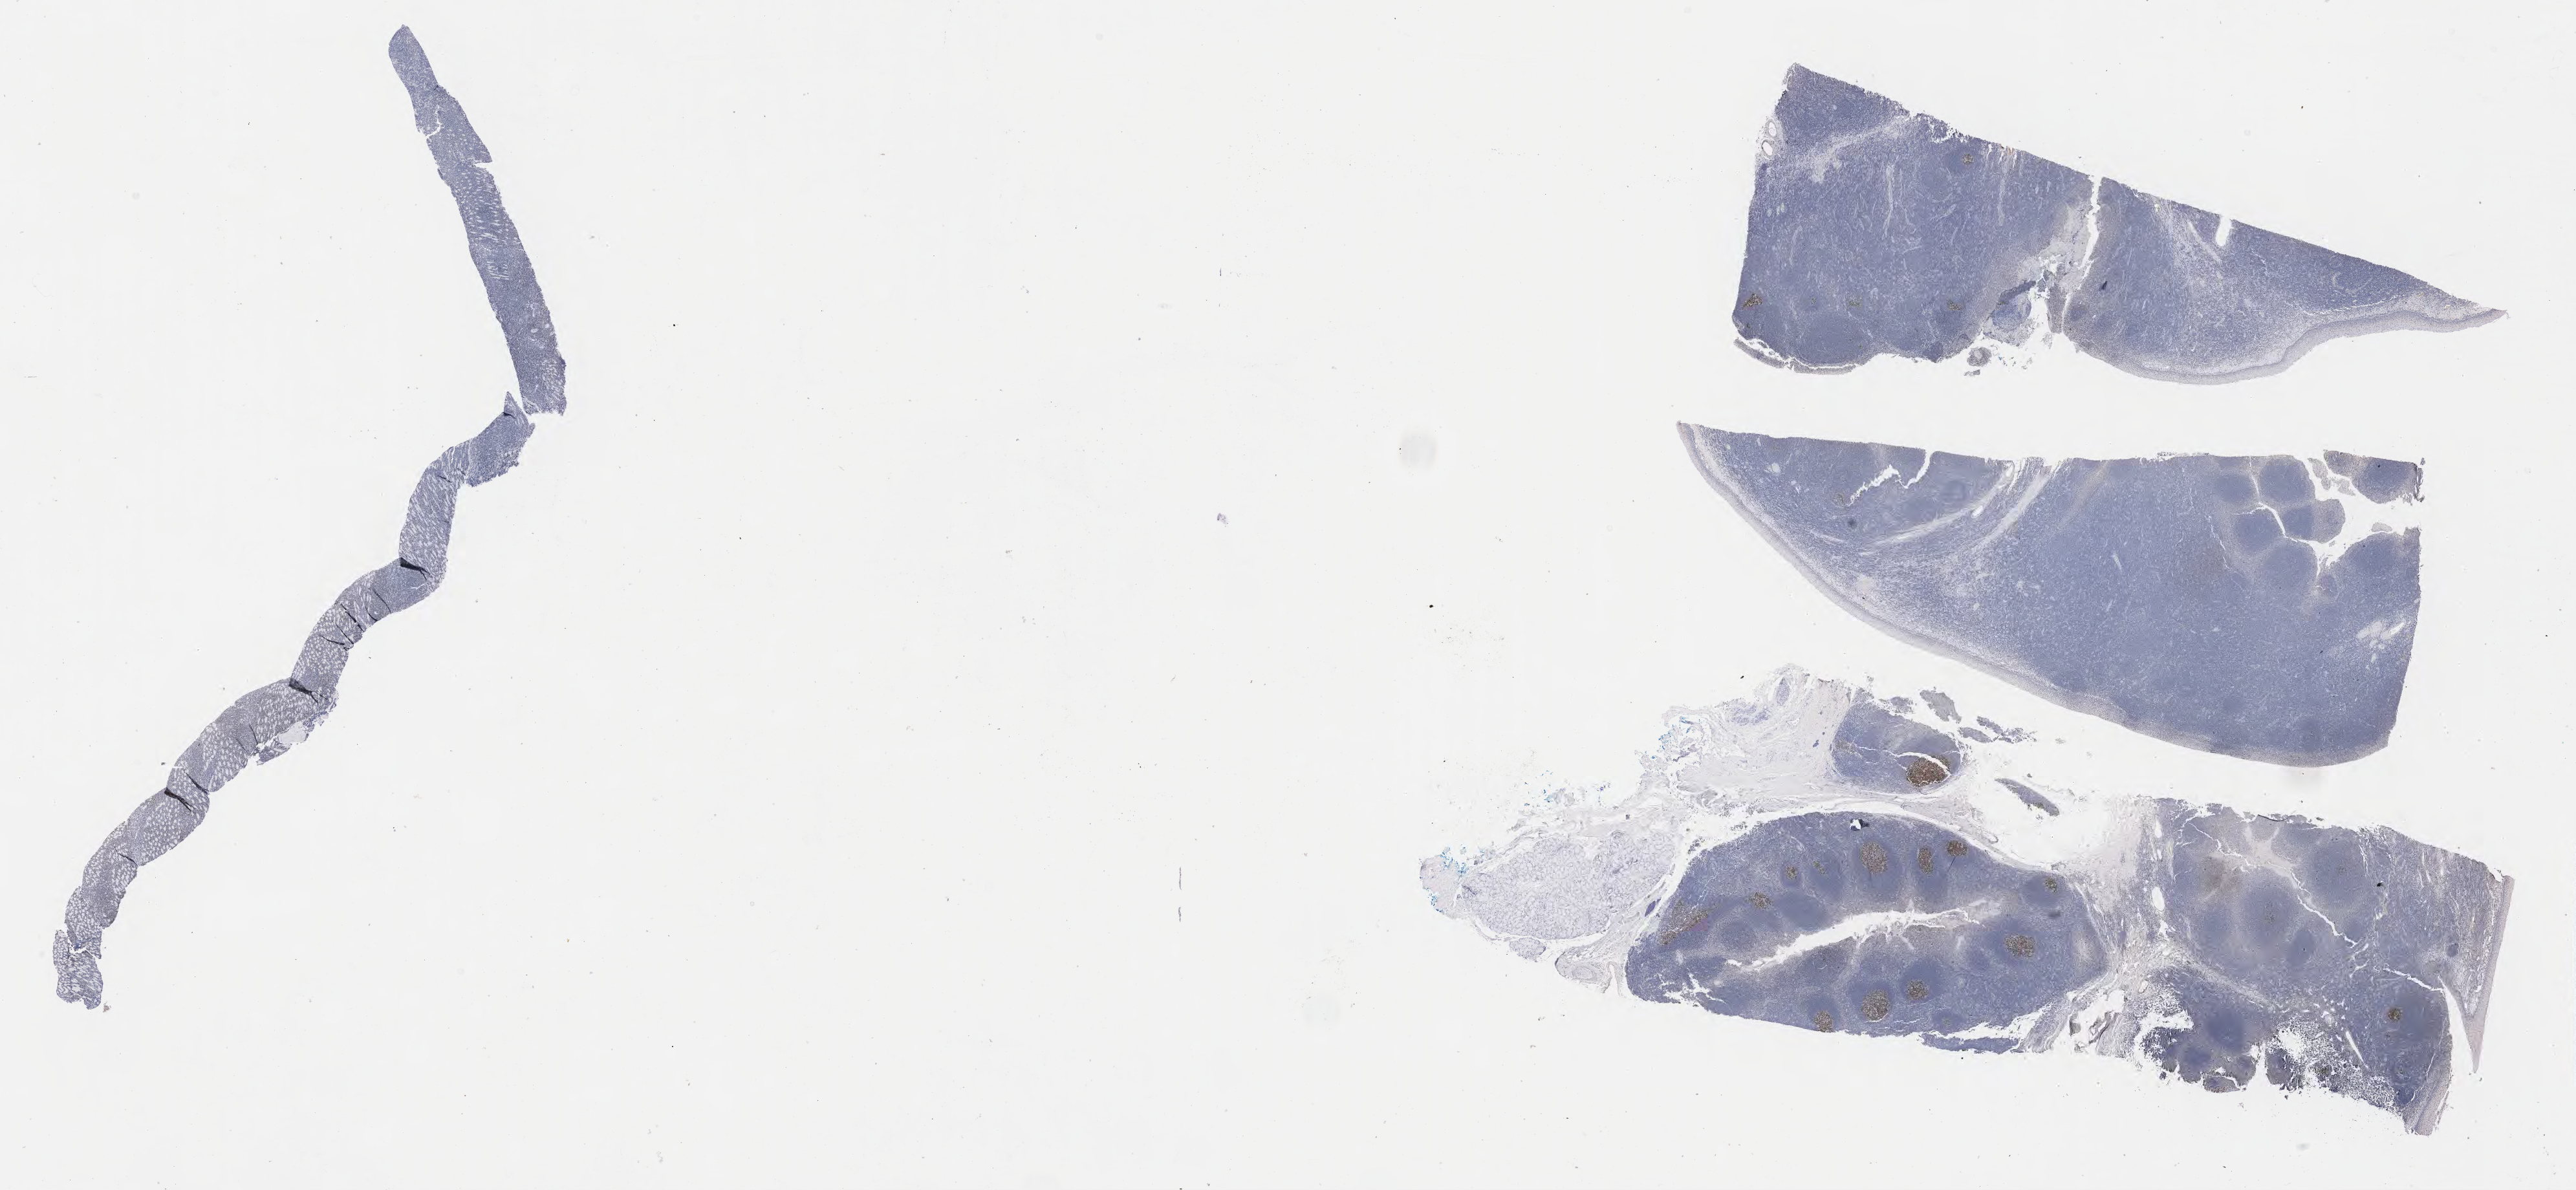
Immunohistochemistry (IHC) whole-slide image stained for BCL6, low-resolution overview of the scanned area, about 32.2 x 14.9 mm, tumor tissue. Male, age 4 years at initial diagnosis.
- diagnosis: Burkitt lymphoma, NOS